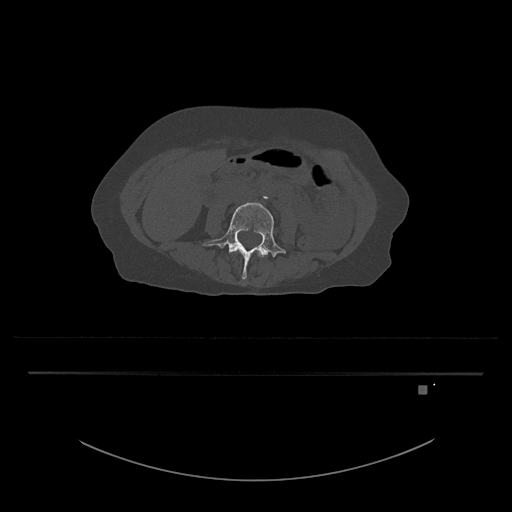
CT including the spine, one axial slice. Slice 371 of 797 in the series (ordered by position). Reconstruction kernel Br40s/3. 120 kVp. Bone window (W 1800 / L 400 HU). 0.5 mm slice thickness. 512 × 512 image matrix, field of view 500 × 500 mm. Female patient, age 57 years. From the clinical record (not read from this slice): primary cancer: cervical.
Outlined on this slice (semi-automatic segmentation, software-assisted and operator-edited):
- L3 vertebra: bounding box (x1, y1, x2, y2) in pixels: (257, 251, 264, 257)
- L4 vertebra: (203, 202, 286, 280)